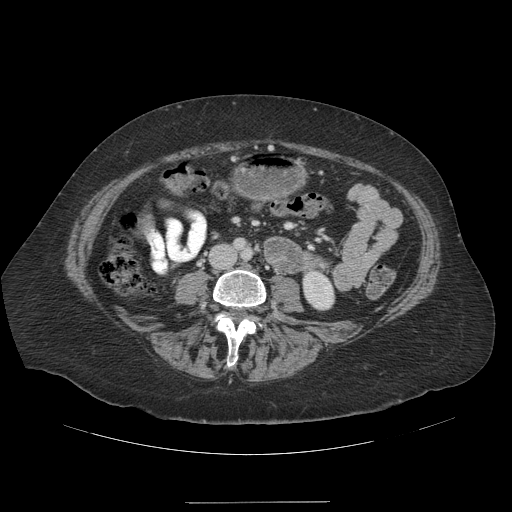
Contrast-enhanced abdominal CT (liver protocol), one axial slice. Slice 26 of 99 in the series (ordered by position). Reconstruction kernel STANDARD. 140 kVp. Soft-tissue window (W 400 / L 40 HU). 512 × 512 image matrix. Case-level facts recorded for this patient, not image findings: diagnosis: hepatocellular carcinoma (patient treated with transarterial chemoembolisation; whether this scan precedes or follows treatment is not stated here); TNM stage (as recorded): Stage-IVA; Child-Pugh class: A.
Outlined on this slice (semi-automatic segmentation, software-assisted and operator-edited):
- liver parenchyma outside the tumour (the mass and vessels are separate outlines, so this box may not span the whole liver): box from (x=146, y=227) to (x=157, y=250) px
- liver vessels: (x=147, y=230)–(x=162, y=249)